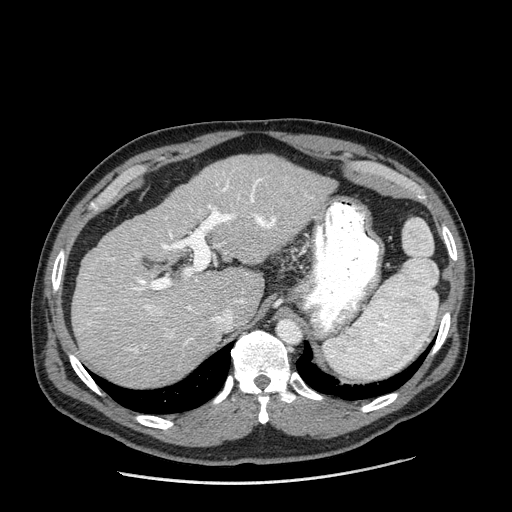
Contrast-enhanced abdominal CT (liver protocol), one axial slice. Position 131 of 198 along the scan axis. Reconstruction kernel STANDARD. 120 kVp. One of 2 acquisitions stored at this slice position. Soft-tissue window (W 400 / L 40 HU). 2.5 mm slice thickness. 512 × 512 image matrix. Case-level facts recorded for this patient, not image findings: diagnosis: hepatocellular carcinoma (patient treated with transarterial chemoembolisation; whether this scan precedes or follows treatment is not stated here); TNM stage (as recorded): Stage-II; Child-Pugh class: A; tumour size: 2.6 cm.
Structures marked on this image (semi-automatic segmentation, software-assisted and operator-edited):
- liver parenchyma outside the tumour (the mass and vessels are separate outlines, so this box may not span the whole liver): box from (x=72, y=154) to (x=334, y=387) px
- liver vessels: (x=88, y=173)–(x=276, y=353)